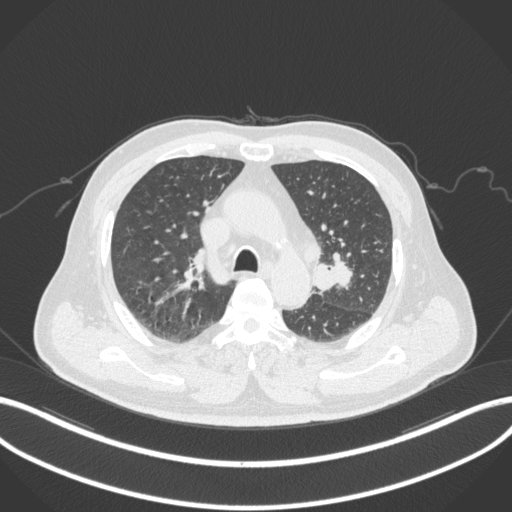
Chest CT, one axial slice; slice 205 of 286 in the series (ordered by position); lung window (W 1500 / L -600 HU); 1 mm slice thickness; 512 × 512 image matrix, field of view 400 × 400 mm. Male patient, age 67 years. Case-level facts recorded for this patient, not image findings: clinical TNM (as recorded): T2a N1 M0; histopathological grade: G3.
Structures marked on this image (rectangle marked by the reading radiologist):
- lung tumour (recorded histology: adenocarcinoma): bounding box [x1, y1, x2, y2] px = [314, 259, 354, 295]